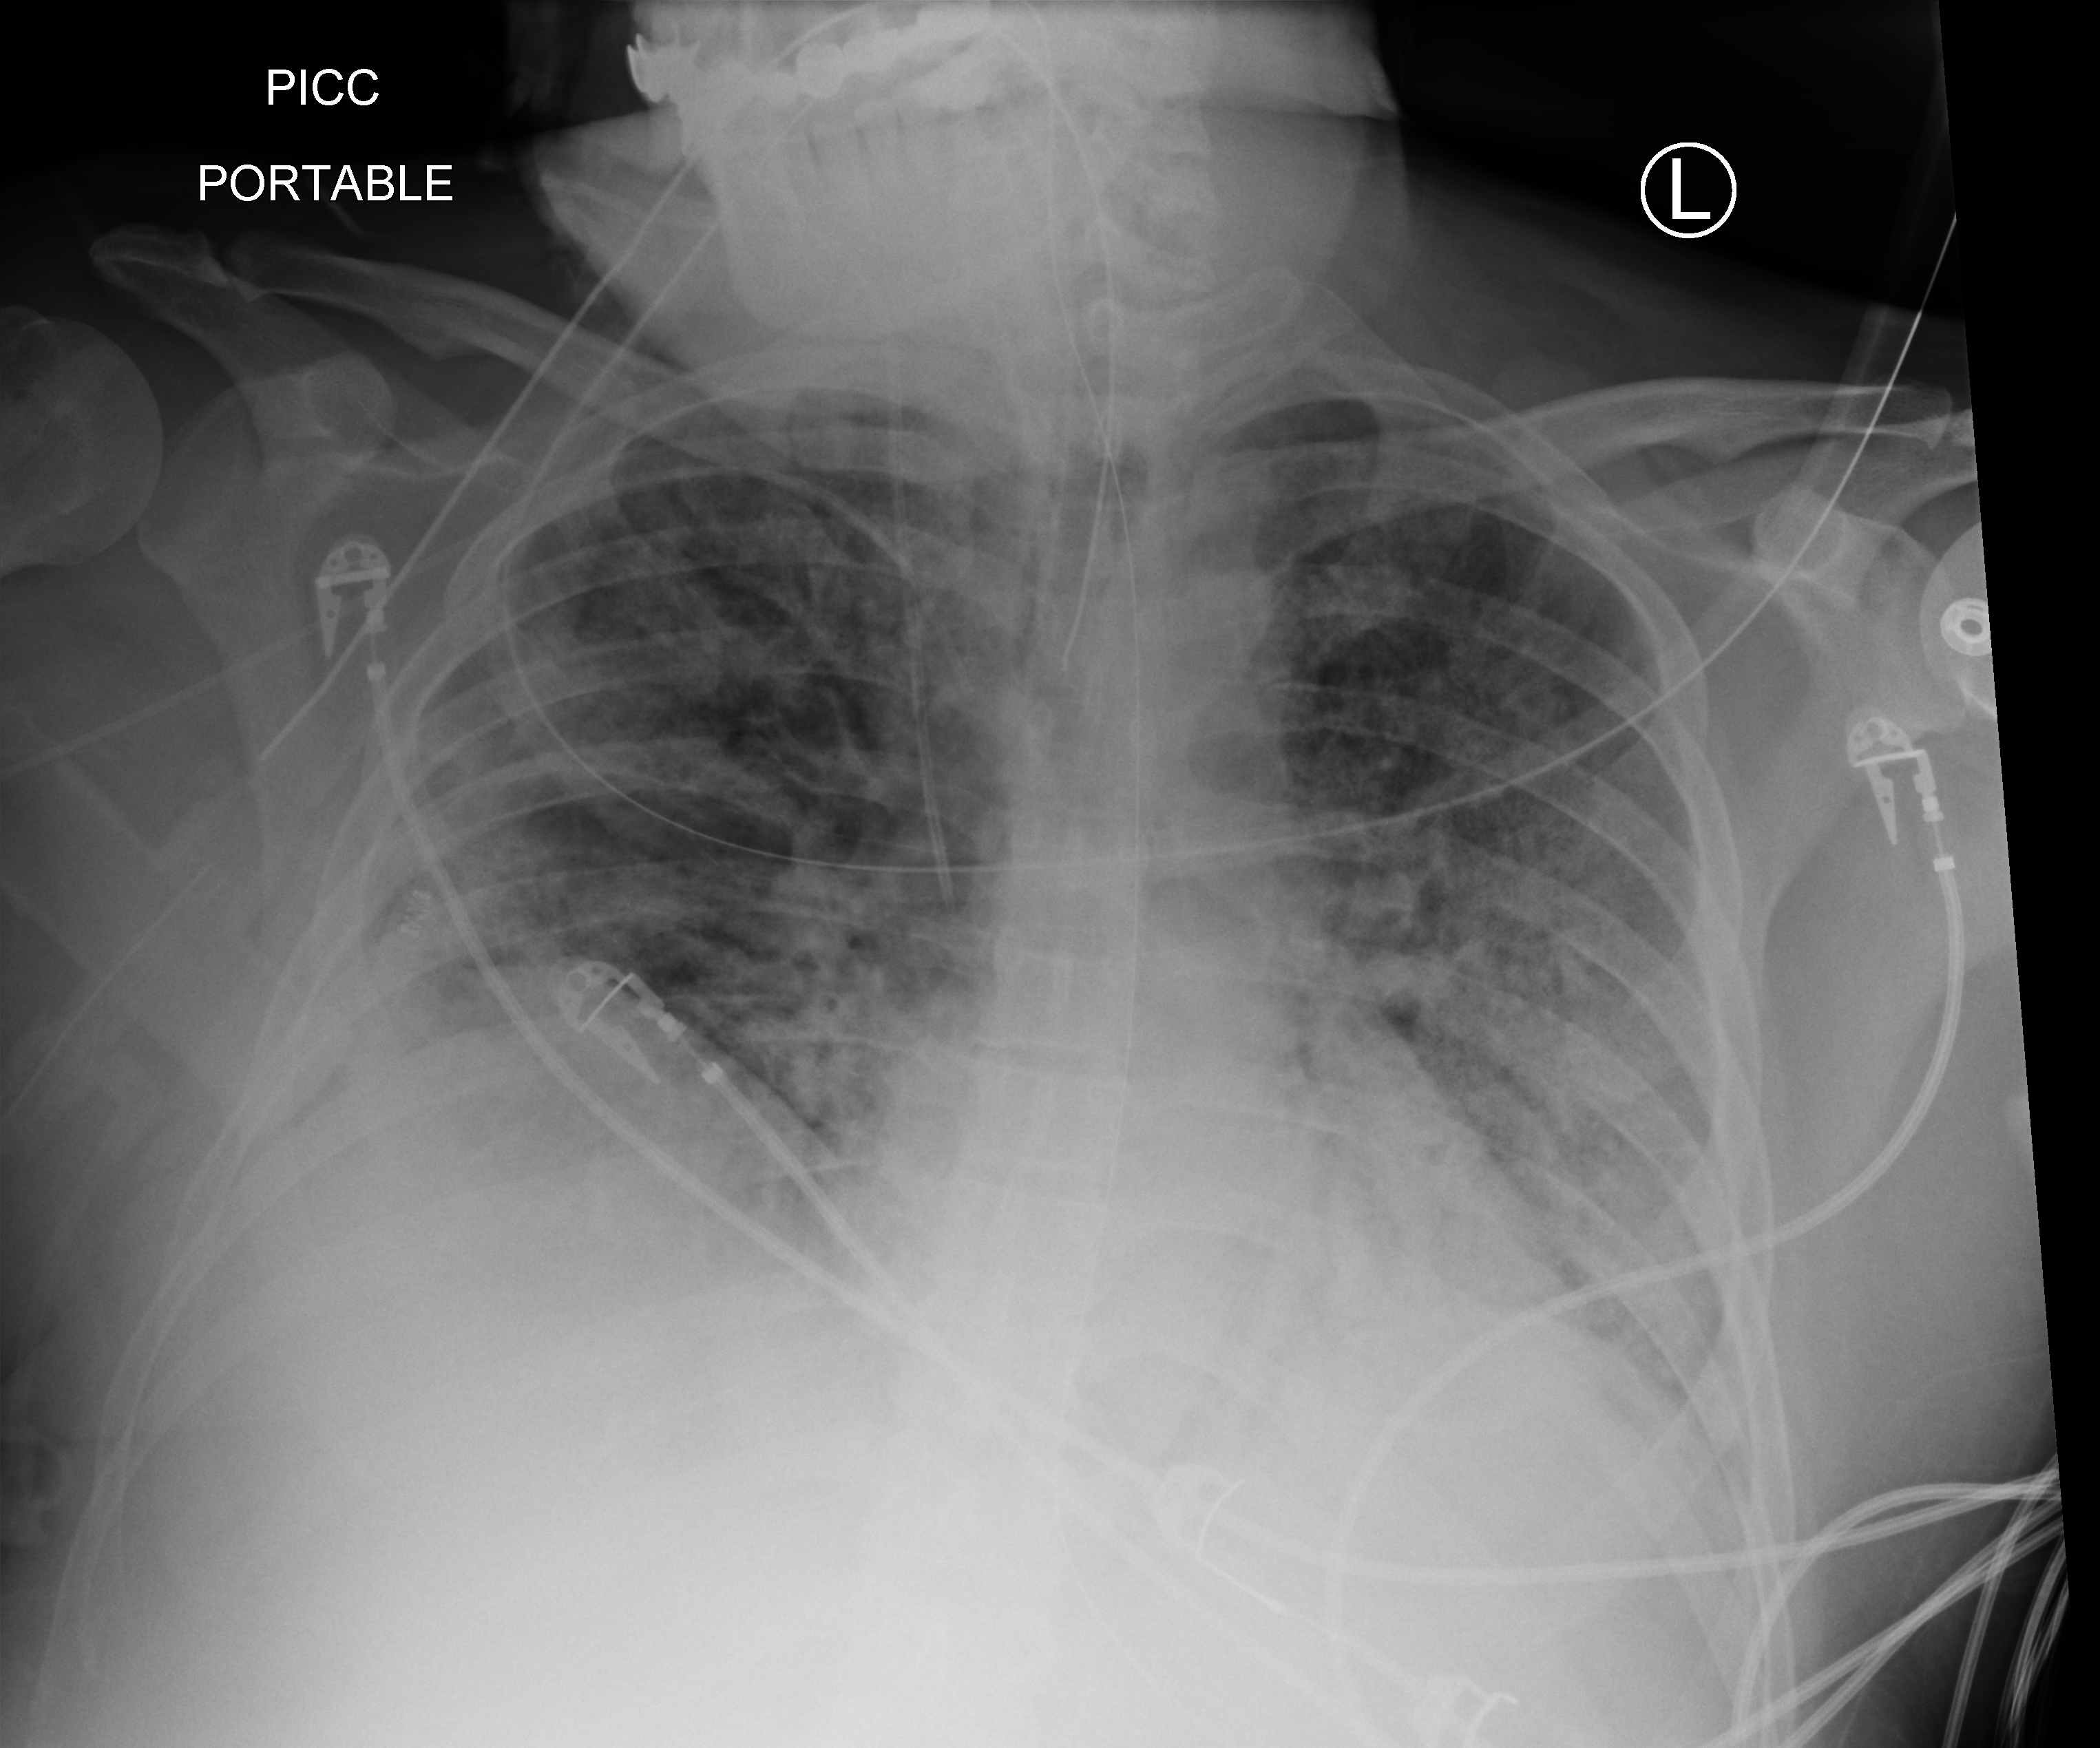
Portable chest radiograph; anteroposterior (AP) projection. Patient hospitalised with COVID-19; male, aged 18–59 years.
Admission-level facts for this patient (not findings on this image; timing relative to this image not recorded): chronic kidney disease (admission record): no; admitted to intensive care during this hospital stay: yes.